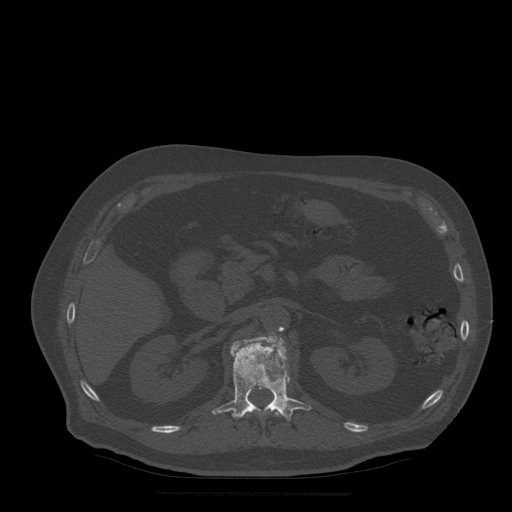
CT including the spine, one axial slice; slice 198 of 522 in the series (ordered by position); bone window (W 1800 / L 400 HU); 512 × 512 image matrix, field of view 420 × 420 mm. Patient age 72 years. From the clinical record (not read from this slice): primary cancer: prostate.
Annotated regions visible in this slice (semi-automatically segmented with operator editing):
- L1 vertebra: bounding box (x1, y1, x2, y2) in pixels: (212, 336, 312, 421)
- T12 vertebra: (247, 410, 278, 417)